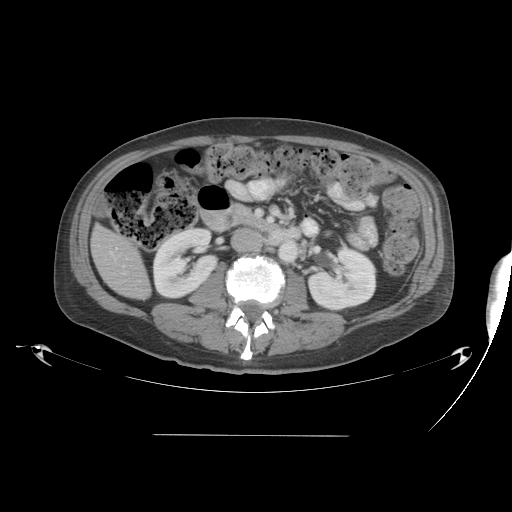
Contrast-enhanced abdominal CT, one axial slice; position 14 of 48 along the scan axis; reconstruction kernel STANDARD; 120 kVp; intravenous contrast given; soft-tissue window (W 400 / L 40 HU); 5 mm slice thickness; 512 × 512 image matrix, field of view 486 × 486 mm. Male patient, age 65 years. From the clinical record (not read from this slice): diagnosis: colorectal cancer liver metastases, imaged before liver resection; multiple liver metastases: yes; largest metastasis: 11 cm; chemotherapy before resection: yes.
Outlined on this slice (outlined manually by an expert reader):
- liver: bounding box [x1, y1, x2, y2] px = [92, 228, 150, 299]